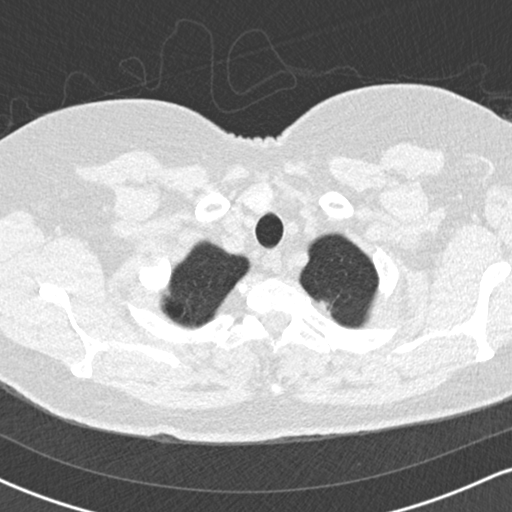
Low-dose screening chest CT, one axial slice. Position 154 of 170 along the scan axis. Lung window (W 1500 / L -600 HU). 512 × 512 image matrix.
Annotated regions visible in this slice (manually delineated by an expert):
- lesion 1 (tumor, upper lobe of left lung): bounding box [x1, y1, x2, y2] px = [320, 301, 330, 314]